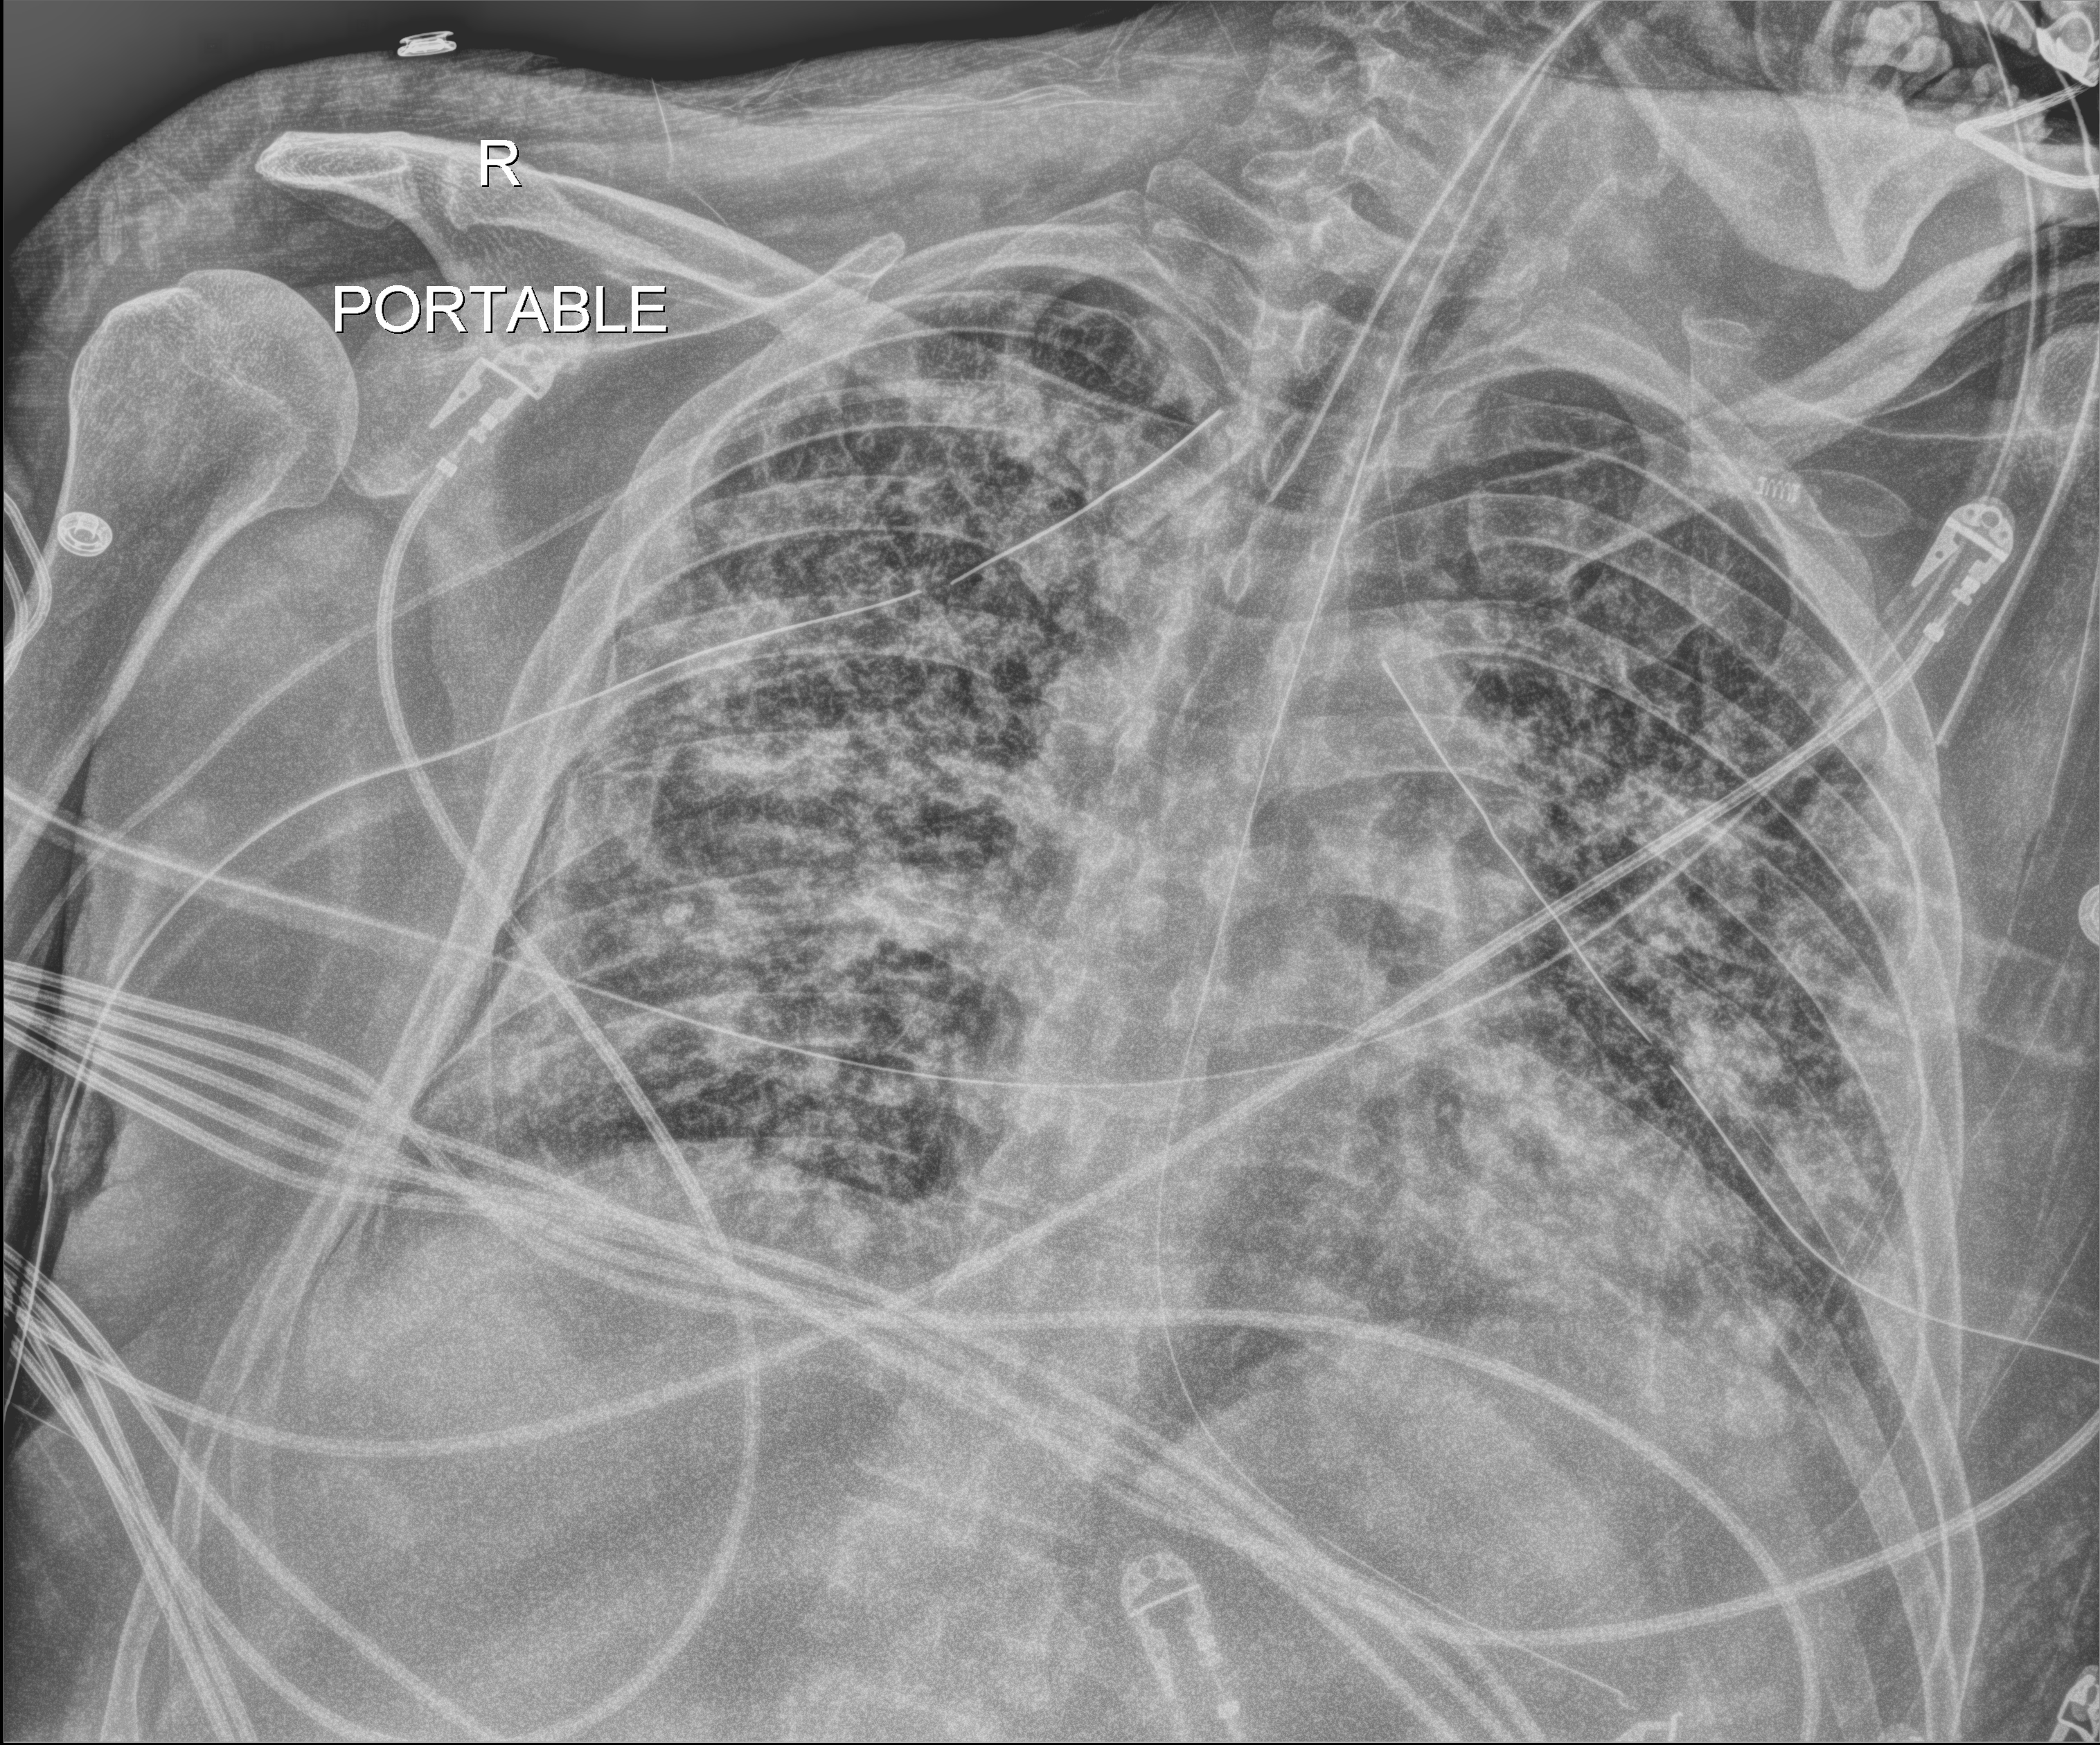
Portable chest radiograph, anteroposterior (AP) projection. Patient hospitalised with COVID-19; male, aged 18–59 years.
From the hospital-stay record, not from the radiograph (when in the stay this image was taken is not recorded):
- admitted to intensive care during this hospital stay: yes